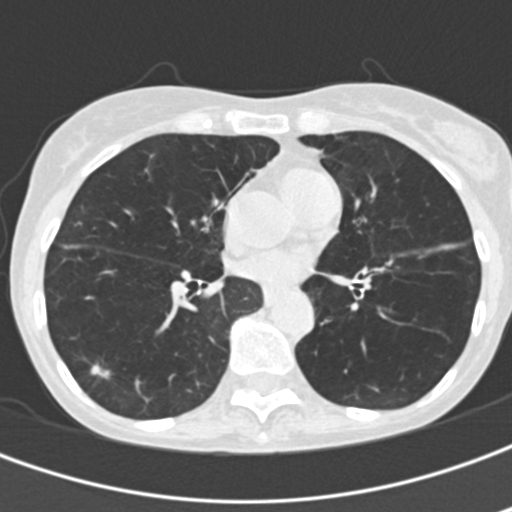
Axial slice from a low-dose chest CT screening exam; second annual screen; lung window (W 1500 / L -600 HU); 2 mm slice thickness; standard (soft-tissue) reconstruction kernel (B30f); slice 100 of 201 in the series; 512 × 512 image matrix, field of view 280 × 280 mm. Female, age 68 years at enrolment. Former smoker at enrolment.
Expert-annotated lung lesion, box from (x=76, y=352) to (x=121, y=388) px. Reader record for this screening exam (exam-level; its link to the box is not recorded): non-calcified nodule or mass ≥4 mm, right lower lobe, 9 × 7 mm, spiculated (stellate) margins, soft tissue attenuation, pre-existing on the prior screen: yes; interval growth: yes. Later outcome: lung cancer diagnosed 659 days after this screen — squamous cell carcinoma, NOS, right lower lobe, stage IA (AJCC 6th edition).